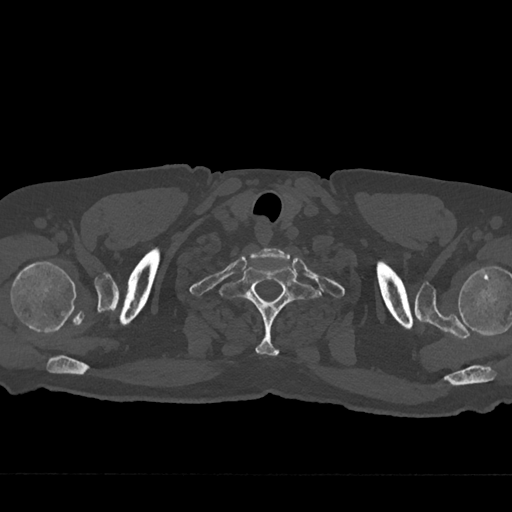
CT including the spine, one axial slice; position 662 of 797 along the scan axis; reconstruction kernel Br40s/3; 120 kVp; bone window (W 1800 / L 400 HU); 512 × 512 image matrix, field of view 377 × 377 mm. Patient: male, 75 years. Case-level facts recorded for this patient, not image findings: primary cancer: renal.
Outlined on this slice (semi-automatic segmentation, software-assisted and operator-edited):
- T1 vertebra: bounding box <218,265,321,356> (left, top, right, bottom; pixels)
- T2 vertebra: <281,292,283,295>